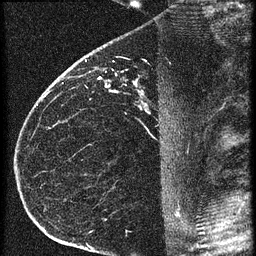
Breast MRI (dynamic contrast-enhanced), one sagittal slice. Slice 40 of 60 in the series (ordered by position). 3 images stored at this slice position (order not interpretable as contrast timing). 1.5 T. TE 4.2 ms, TR 20.4 ms. 256 × 256 image matrix, field of view 180 × 180 mm. Patient: female, 35 years. Case-level facts recorded for this patient, not image findings: setting: breast cancer imaged before/during neoadjuvant chemotherapy; receptor status: HR-positive, HER2-negative.
Outlined on this slice (semi-automatic segmentation, software-assisted and operator-edited):
- analysis volume of interest (the breast-tissue region the enhancement analysis was run in; not a lesion): bounding box <65,60,169,119> (left, top, right, bottom; pixels)
- tumour enhancement mask (voxels above the 90 % enhancement threshold inside the analysis volume of interest): <98,78,146,107>